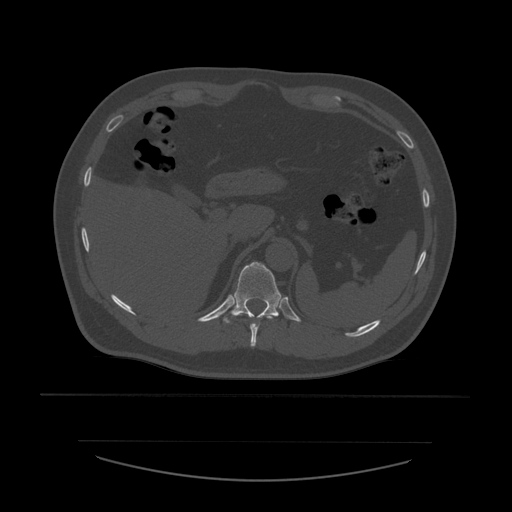
CT including the spine, one axial slice. Position 282 of 532 along the scan axis. 120 kVp. Bone window (W 1800 / L 400 HU). 512 × 512 image matrix, field of view 441 × 441 mm. Patient age 44 years. Case-level facts recorded for this patient, not image findings: primary cancer: soft tissue sarcoma.
Structures marked on this image (semi-automatically segmented with operator editing):
- T10 vertebra: box from (x=250, y=316) to (x=273, y=347) px
- T11 vertebra: (x=224, y=262)–(x=282, y=324)